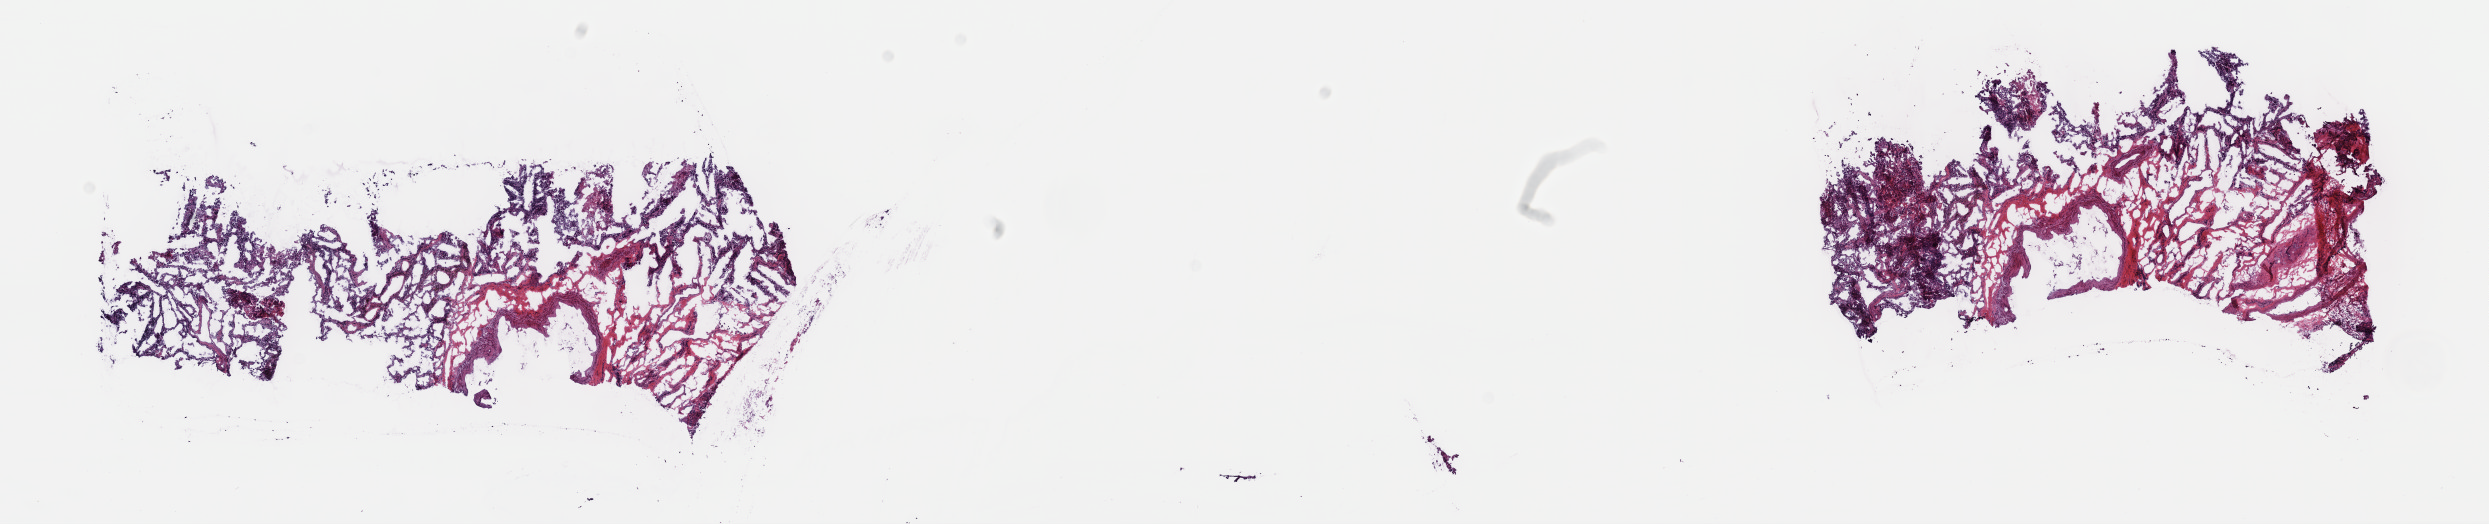
Digitized Hematoxylin and eosin (H&E) stained tissue section (whole slide) — low-resolution overview of the scanned area, about 20.1 x 4.2 mm. Frozen section from the top of the tissue portion. Sample: primary tumour, lung. Female patient; age at initial diagnosis 51 years. Composition of this section per pathologist review: tumour cells 60%, tumour nuclei 60%, normal cells 0%, stromal cells 40%, necrosis 0%. Infiltration values recorded for this section: lymphocyte infiltration 0%, monocyte infiltration 0%, neutrophil infiltration 0%.
AJCC pathologic stage: IA. Diagnosis: Adenocarcinoma, NOS (upper lobe, lung). Laterality: right. TNM: T1 N0 MX.